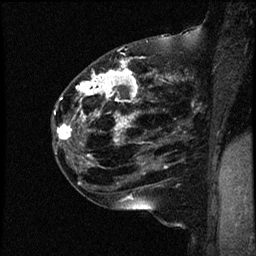
Breast MRI (dynamic contrast-enhanced), one sagittal slice; slice 30 of 44 in the series (ordered by position); dynamic contrast-enhanced study with each time point stored as its own series, time point 2 of 4 at this slice position (early post-contrast, ordered by acquisition time); 1.5 T; TE 4.2 ms, TR 17.7 ms; 2 mm slice thickness; 256 × 256 image matrix, field of view 200 × 200 mm. Female patient, age 52 years. Case-level facts recorded for this patient, not image findings: setting: breast cancer imaged before/during neoadjuvant chemotherapy; receptor status: HR-positive, HER2-negative.
Structures marked on this image (semi-automatically segmented with operator editing):
- analysis volume of interest (the breast-tissue region the enhancement analysis was run in; not a lesion): box from (x=52, y=48) to (x=163, y=147) px
- tumour enhancement mask (voxels above the 100 % enhancement threshold inside the analysis volume of interest): (x=57, y=48)–(x=137, y=144)